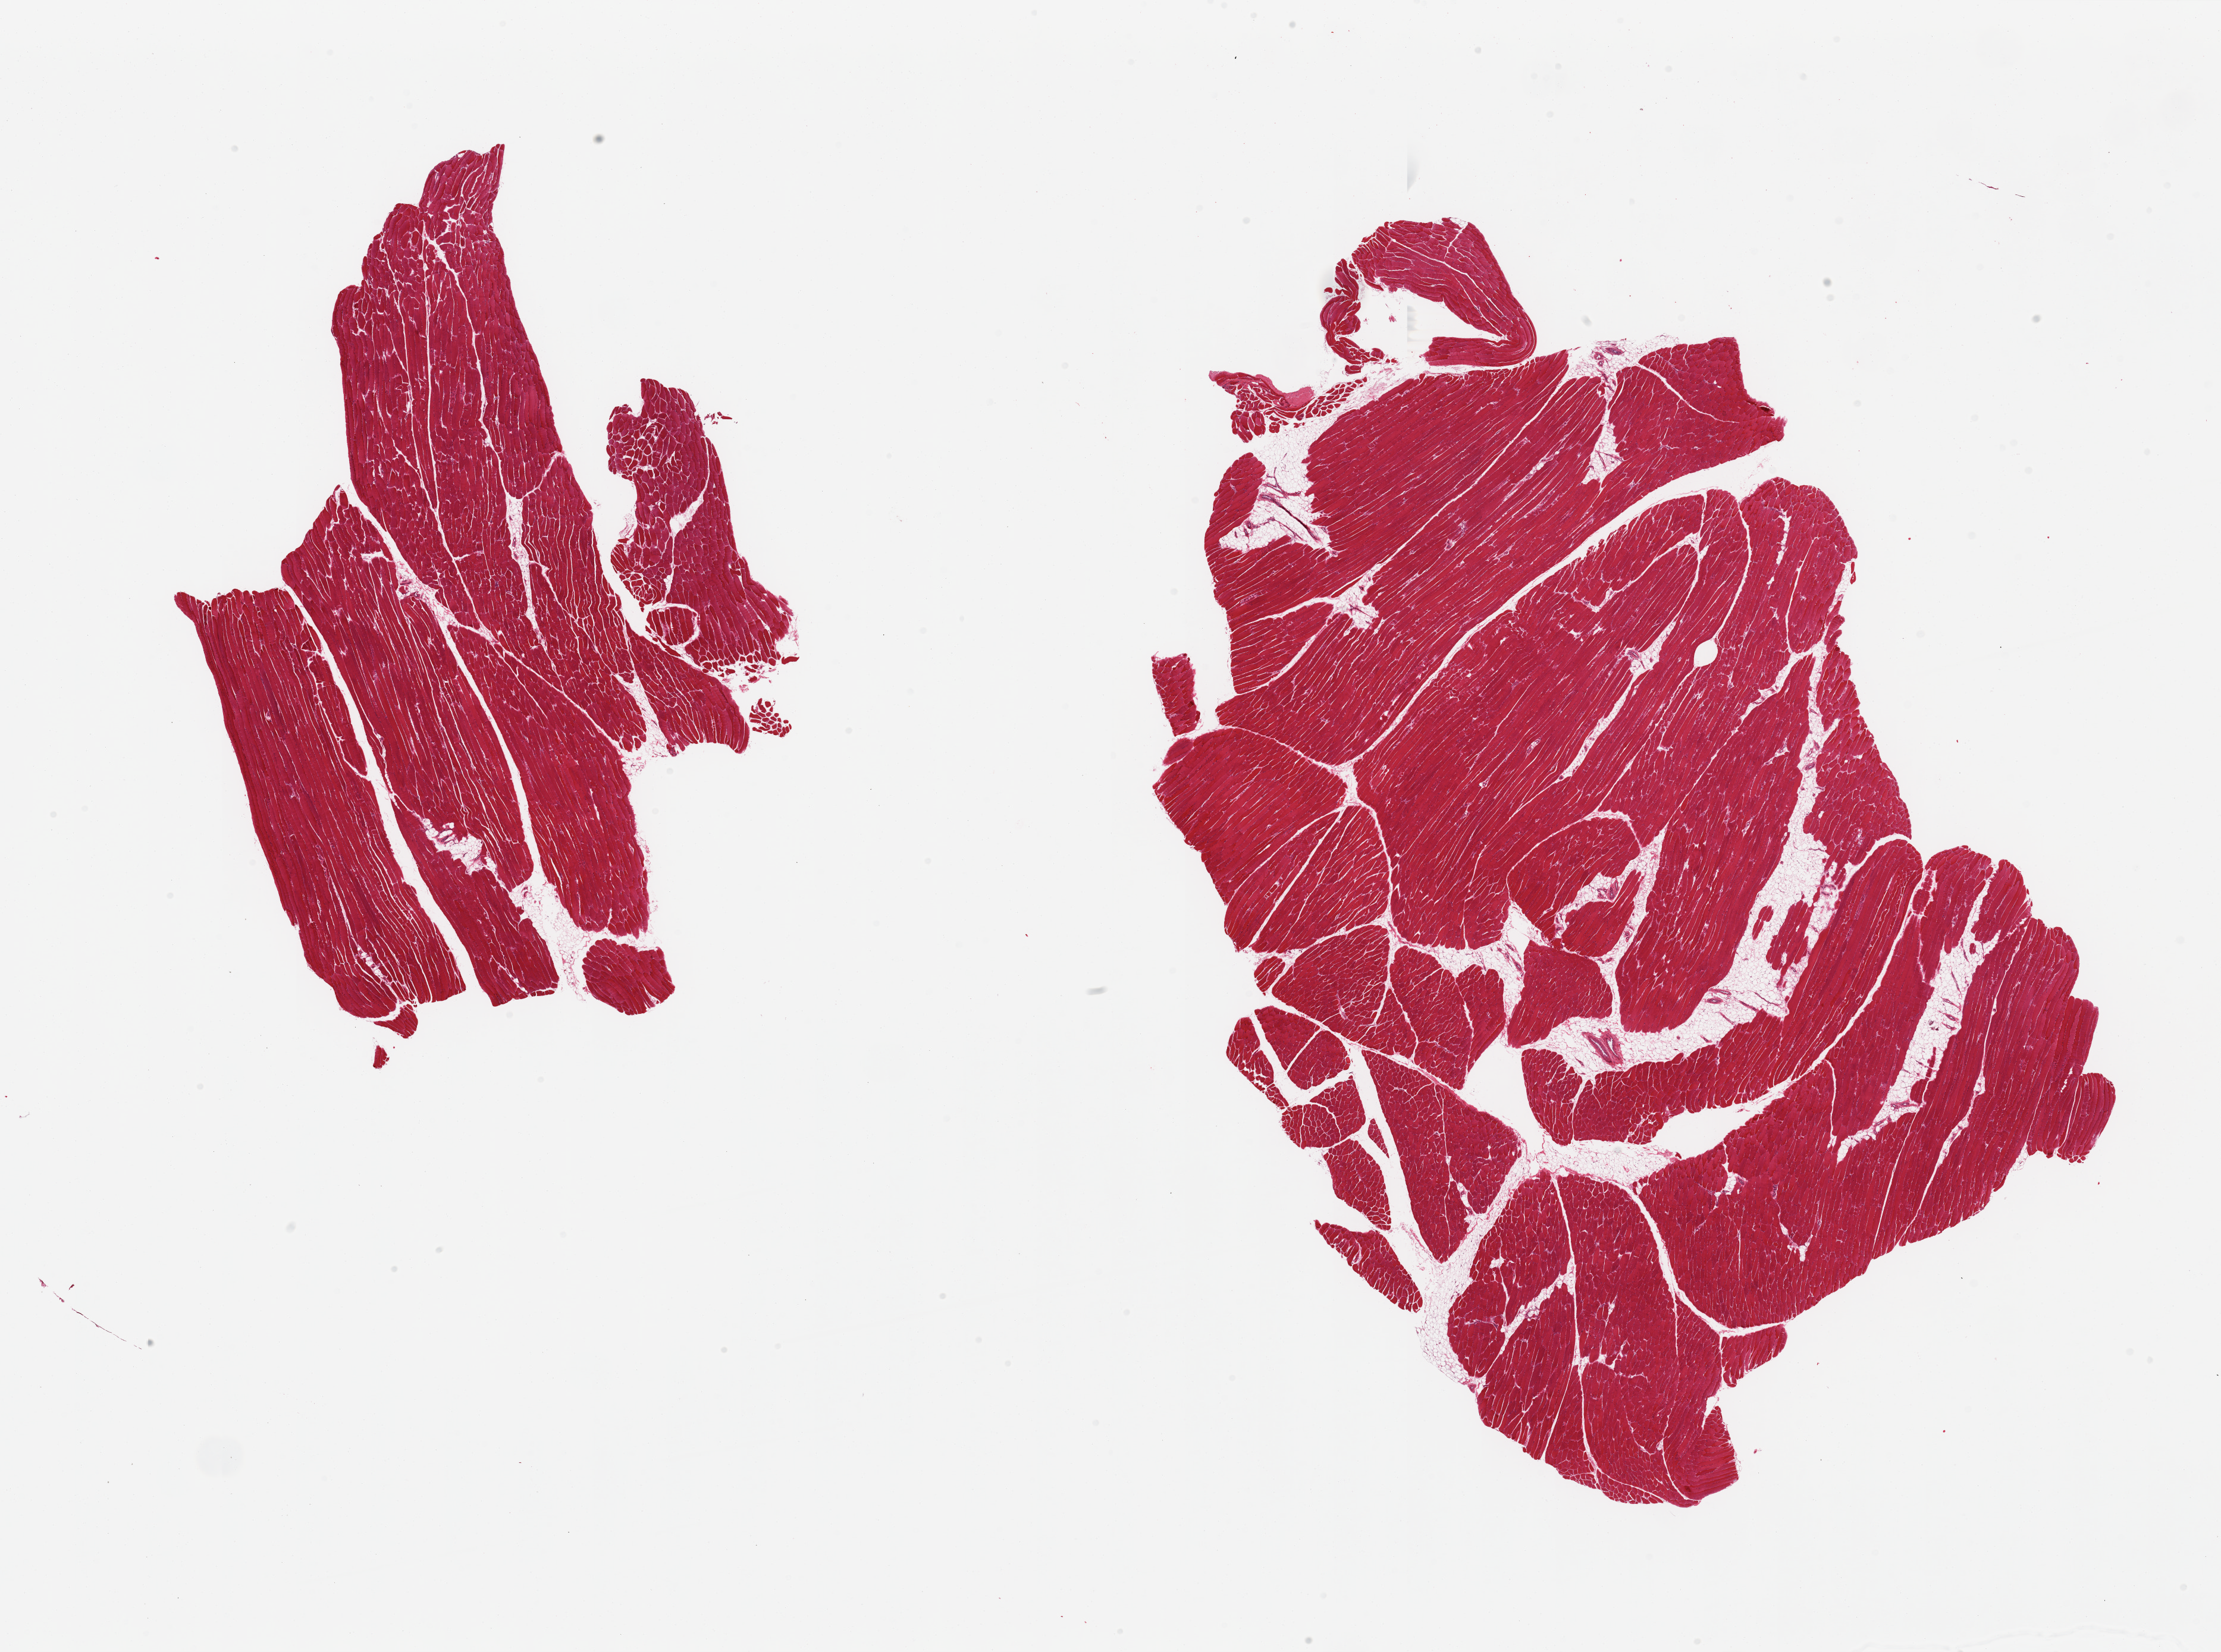
Hematoxylin and eosin (H&E) whole-slide image, brightfield — low-resolution overview of the scanned area, about 29.5 x 22.0 mm (acquisition: 20x scan); PAXgene-fixed paraffin-embedded (PFPE) section; section of skeletal muscle (target tissue); tissue donor sample. Donor: male.
* reviewer comment on this tissue sample: 2 pieces; 10% internal fat